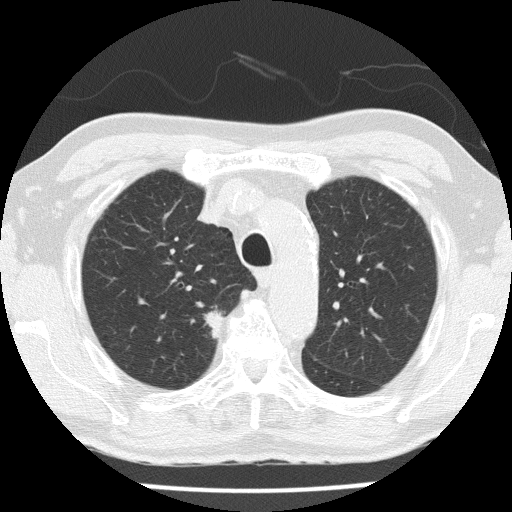
Axial slice from a low-dose chest CT screening exam. Third screening round (two years after baseline). Lung window (W 1500 / L -600 HU). 2 mm slice thickness. Slice 42 of 153 in the series. 512 × 512 image matrix, field of view 323 × 323 mm. Male participant, aged 72 years at enrolment. Current smoker at enrolment.
Lesion marked by an expert reader, box from (x=187, y=298) to (x=237, y=348) px. The exam's reader record, not a measurement of the box and not confirmed to be the same lesion: non-calcified nodule or mass ≥4 mm, right upper lobe, 14 × 14 mm, spiculated (stellate) margins, soft tissue attenuation, pre-existing on the prior screen: yes; interval growth: yes. Participant outcome: lung cancer diagnosed 67 days after this screen — squamous cell carcinoma, NOS, right upper lobe, moderately differentiated (G2), stage IIA (AJCC 6th edition), 25 mm at pathology.